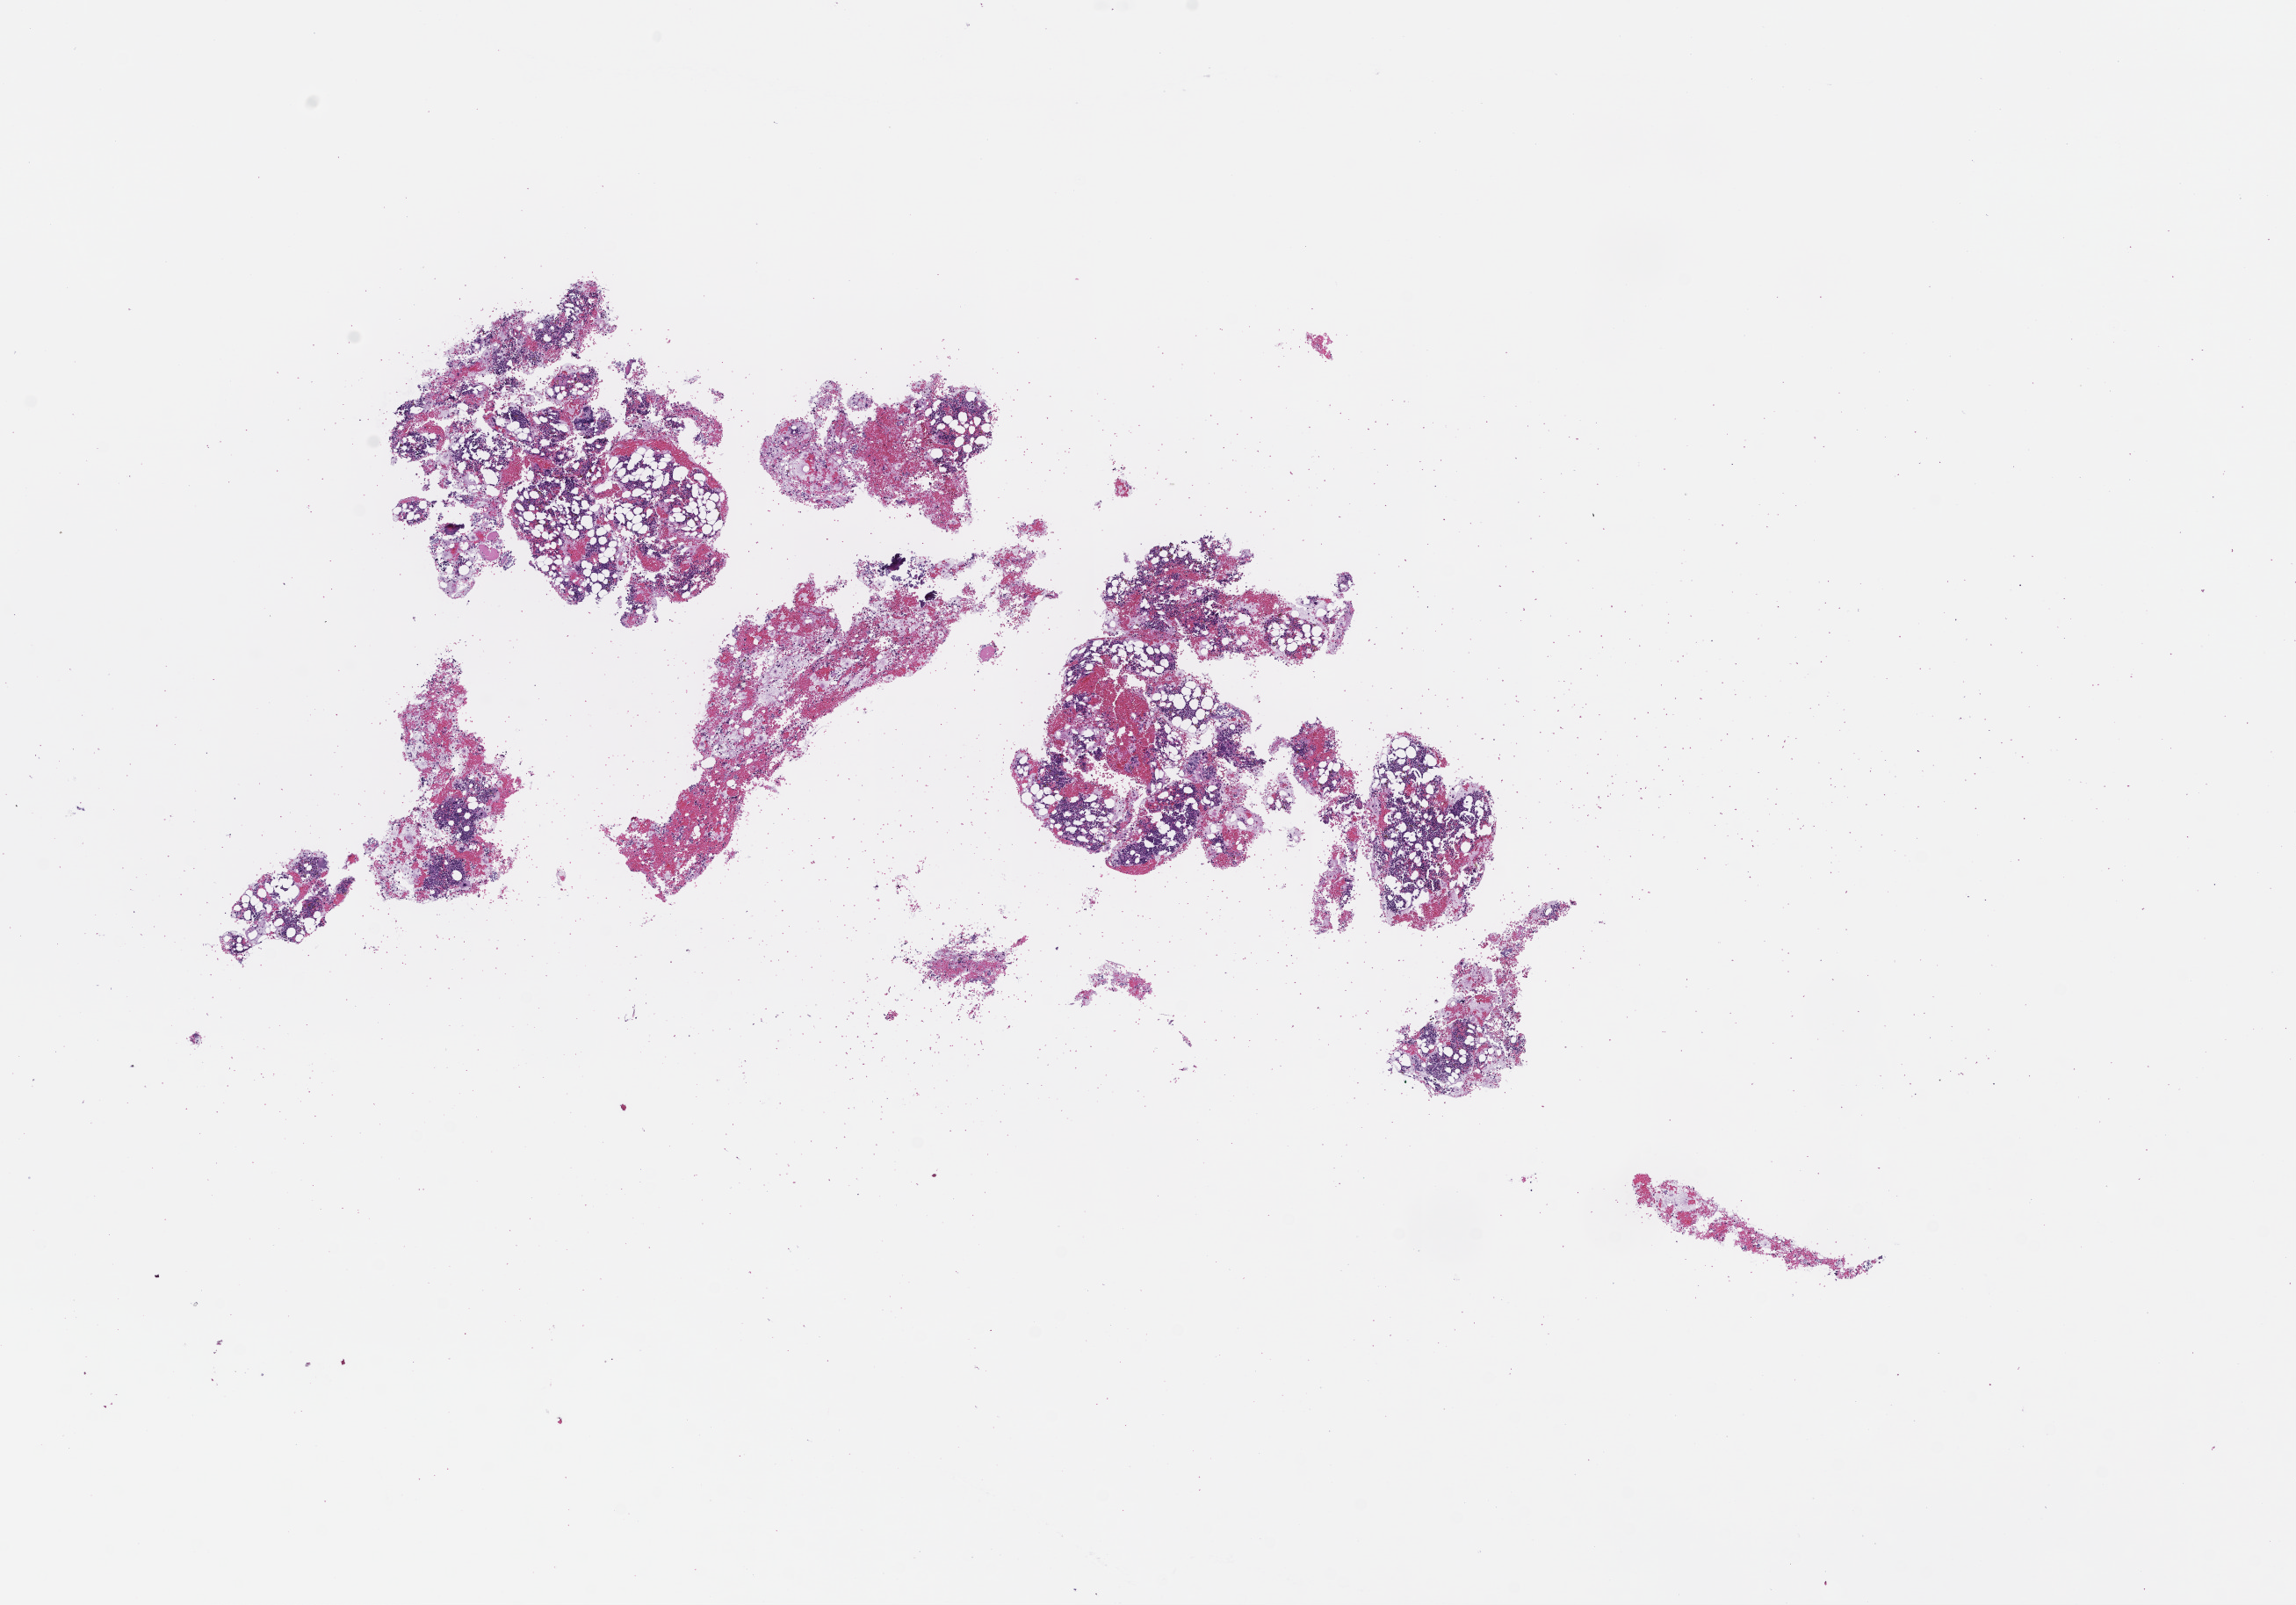
Digitized H&E-stained section, whole scanned area (about 10.6 x 7.4 mm) shown as a low-resolution overview; FFPE section; site: bone marrow; specimen time point: collected at disease progression. Patient: female.
This section: primary tumor. Diagnosis: Acute Myeloid Leukemia Not Otherwise Specified.